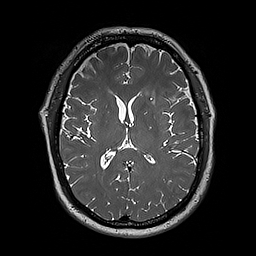
Brain MRI from a brain-tumour surgery series, one axial slice. 256 × 256 image matrix. From the clinical record (not read from this slice): histopathology: Oligodendroglioma; WHO grade: 3; IDH mutation: yes; tumour location: Left Sylvian Fissure (Temporal).
Annotated regions visible in this slice (manually delineated by an expert):
- tumour: bounding box [x1, y1, x2, y2] px = [144, 84, 187, 115]